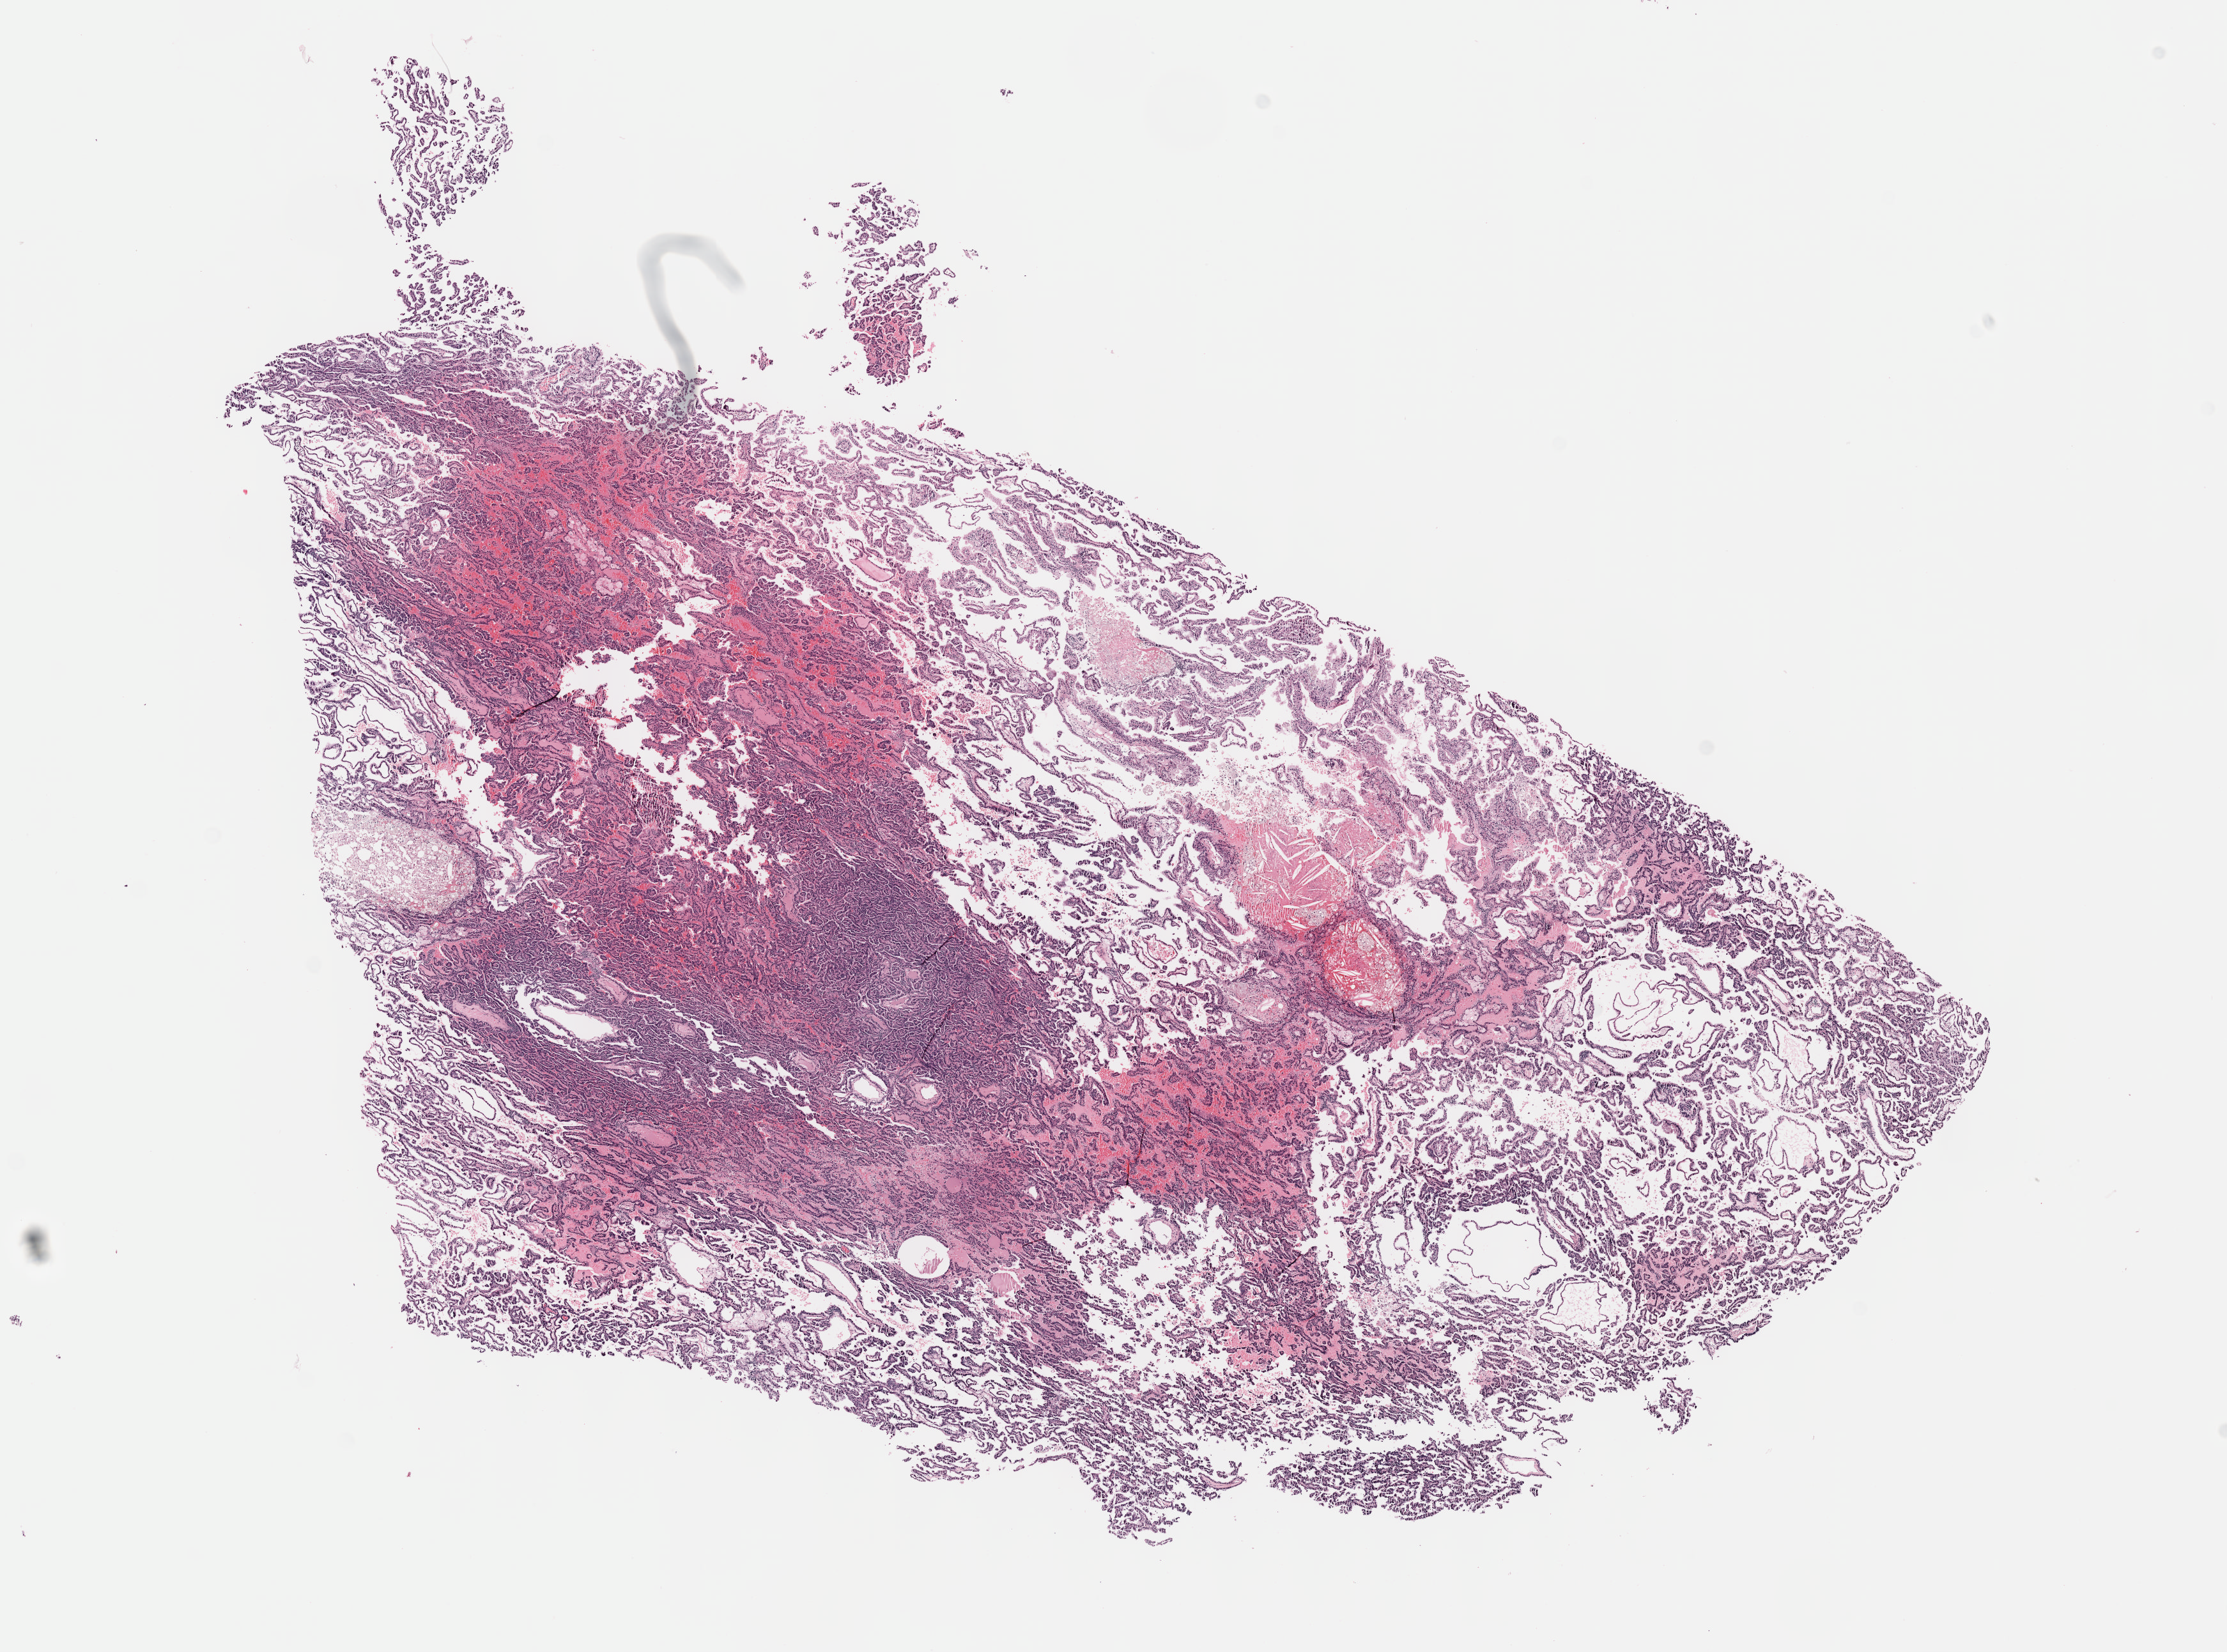
Digitized H&E tissue section (whole slide), whole scanned area (about 14.1 x 10.5 mm, acquisition: 40x scan) shown as a low-resolution overview. Formalin-fixed paraffin-embedded (FFPE) diagnostic section. Primary tumour sample from the kidney. Male, age 74 years at initial diagnosis.
AJCC pathologic stage: II (6th edition). Diagnosis: Papillary adenocarcinoma, NOS.